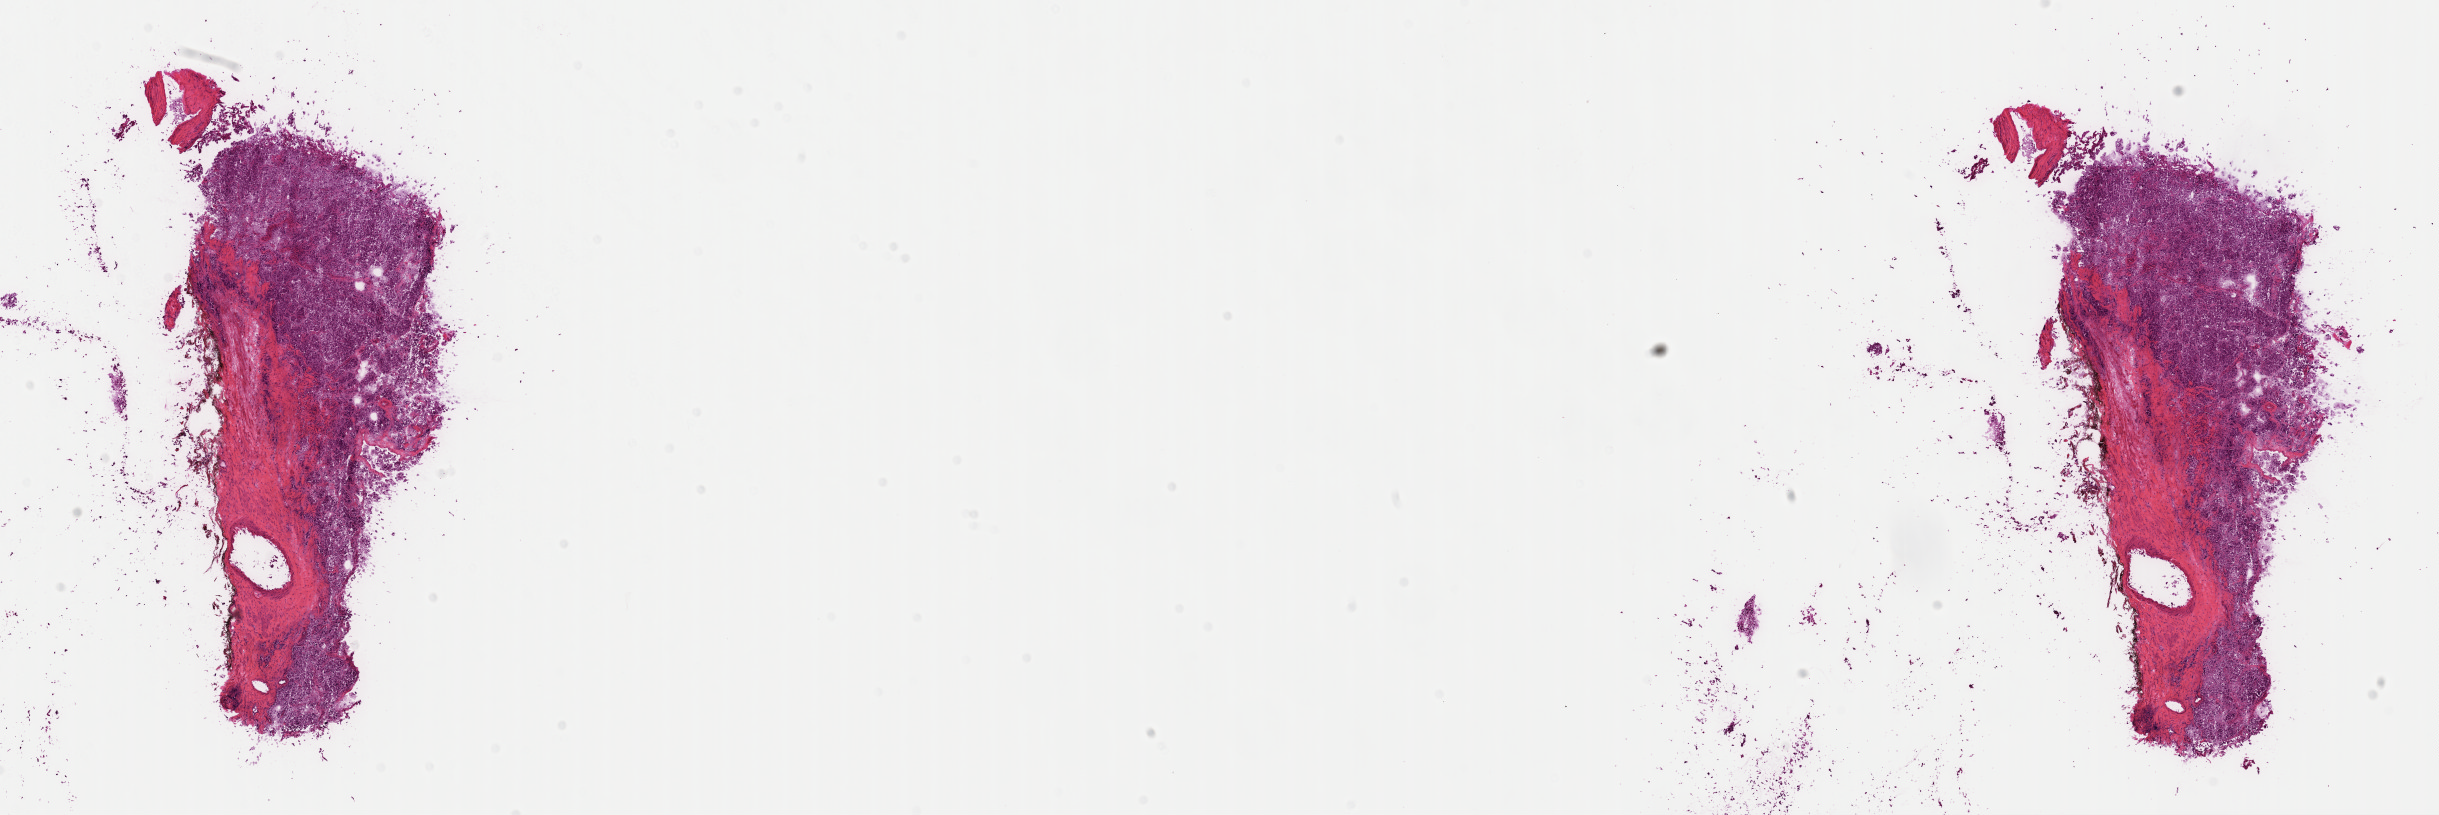
H&E whole-slide image, low-resolution overview of the scanned area, about 19.3 x 6.4 mm; frozen section from the top of the tissue portion; connective, subcutaneous and other soft tissues, primary tumour sample. Female patient; age at initial diagnosis 39 years. Slide review estimates, as recorded: tumour cells 65%, tumour nuclei 90%, normal cells 0%, stromal cells 35%, necrosis 0%. Infiltration values recorded for this section: lymphocyte infiltration 0%, monocyte infiltration 0%, neutrophil infiltration 0%.
- pathologic diagnosis: Aortic body tumor (connective, subcutaneous and other soft tissues of thorax)
- lymph nodes positive (case pathology): 0 of 10 examined